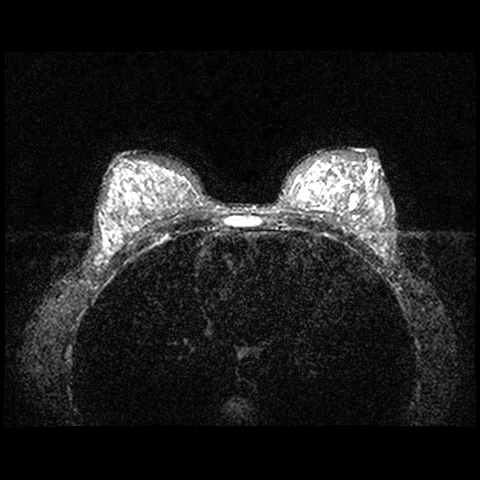
Breast MRI examination; 2 images, each one mid-volume slice chosen by position. Age decade 20s.
Image 1: fluid-sensitive (T2/STIR) axial slice, series "STIR SENSE", slice 43 of 84, 2 mm slice thickness.
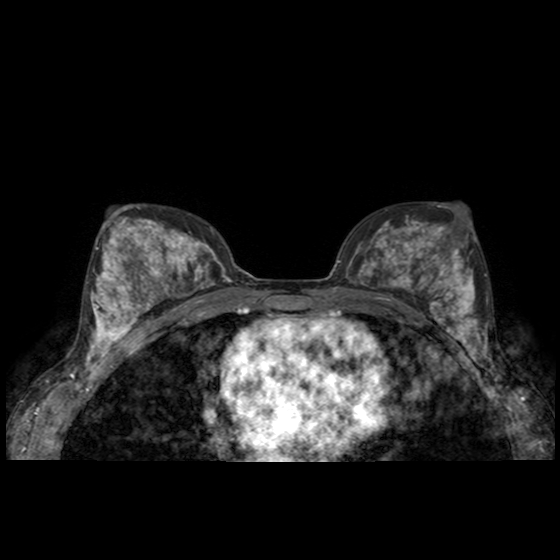
Image 2: post-contrast dynamic axial slice, series "AX BLISS_AUTO SENSE", slice 43 of 84, dynamic phase 5 of 8.
MRI impression (as recorded): Numerous scattered bilateral simple cysts are seen, some of which are clustered, consistent with fibrocystic changes. LEFT BREAST: There is extreme background enhancement. There is an enhancing nodular lesion which measures 1.9 x 1.2 x 2 cm within the centro-lateral right breast (series 401-image 37, dynamic post-contrast slice 72) with a malignant enhancing pattern. This lesion correlates with patient's biopsy-proven cancer. Additionally, approximately 2.5 cm posterior and 1 cm inferior to the patient's known cancer, there is another nodular enhancing lesion which measures up to 1.4 x 0.4 x 1.3 cm. This lesion shows an indeterminate mixed pattern (part of if might be vascular) enhancement, however it is highly suspicious for satellite malignant lesion given its geographic-nodular morphology. No evidence of pectoral muscle infiltration. Normal benign-appearing right axillary lymph nodes are seen with no suspicious enlargement. There is no skin thickening, nipple inversion, or left axillary lymphadenopathy present. Incidental note also made of expected post biopsy findings just anterior to the known malignant lesion. RIGHT BREAST: There is extreme background enhancement. No foci of suspicious enhancement, masses, or areas of architectural distortion seen within the right breast. There is no skin thickening, nipple inversion, or right axillary lymphadenopathy present. IMPRESSION: 1) Suspicious enhancing lesion within the centro-lateral right breast, consistent with patient's known biopsy-proven breast cancer, as detailed above. 2) Additional suspicious nodular area of mixed enhancement a possible second focus of cancer, posterior to the known malignant lesion, as described above. The indeterminate pattern of enhancement suggests the possibility of this representing a vascular structure. However, its nodular geographic morphology makes it highly suspicious for a malignant satellite lesion. 3) Fibrocystic changes within bilateral breasts; BI-RADS 6.
Pathology recorded for this patient (not read from these images): pathology diagnosis: Invasive ductal carcinoma, modified Scarff-Bloom-Richardson grade II/III. No intraductal carcinoma component seen. (right breast); receptor status (as recorded): ER pos (strong), PR pos (strong), HER2 neg (weak).